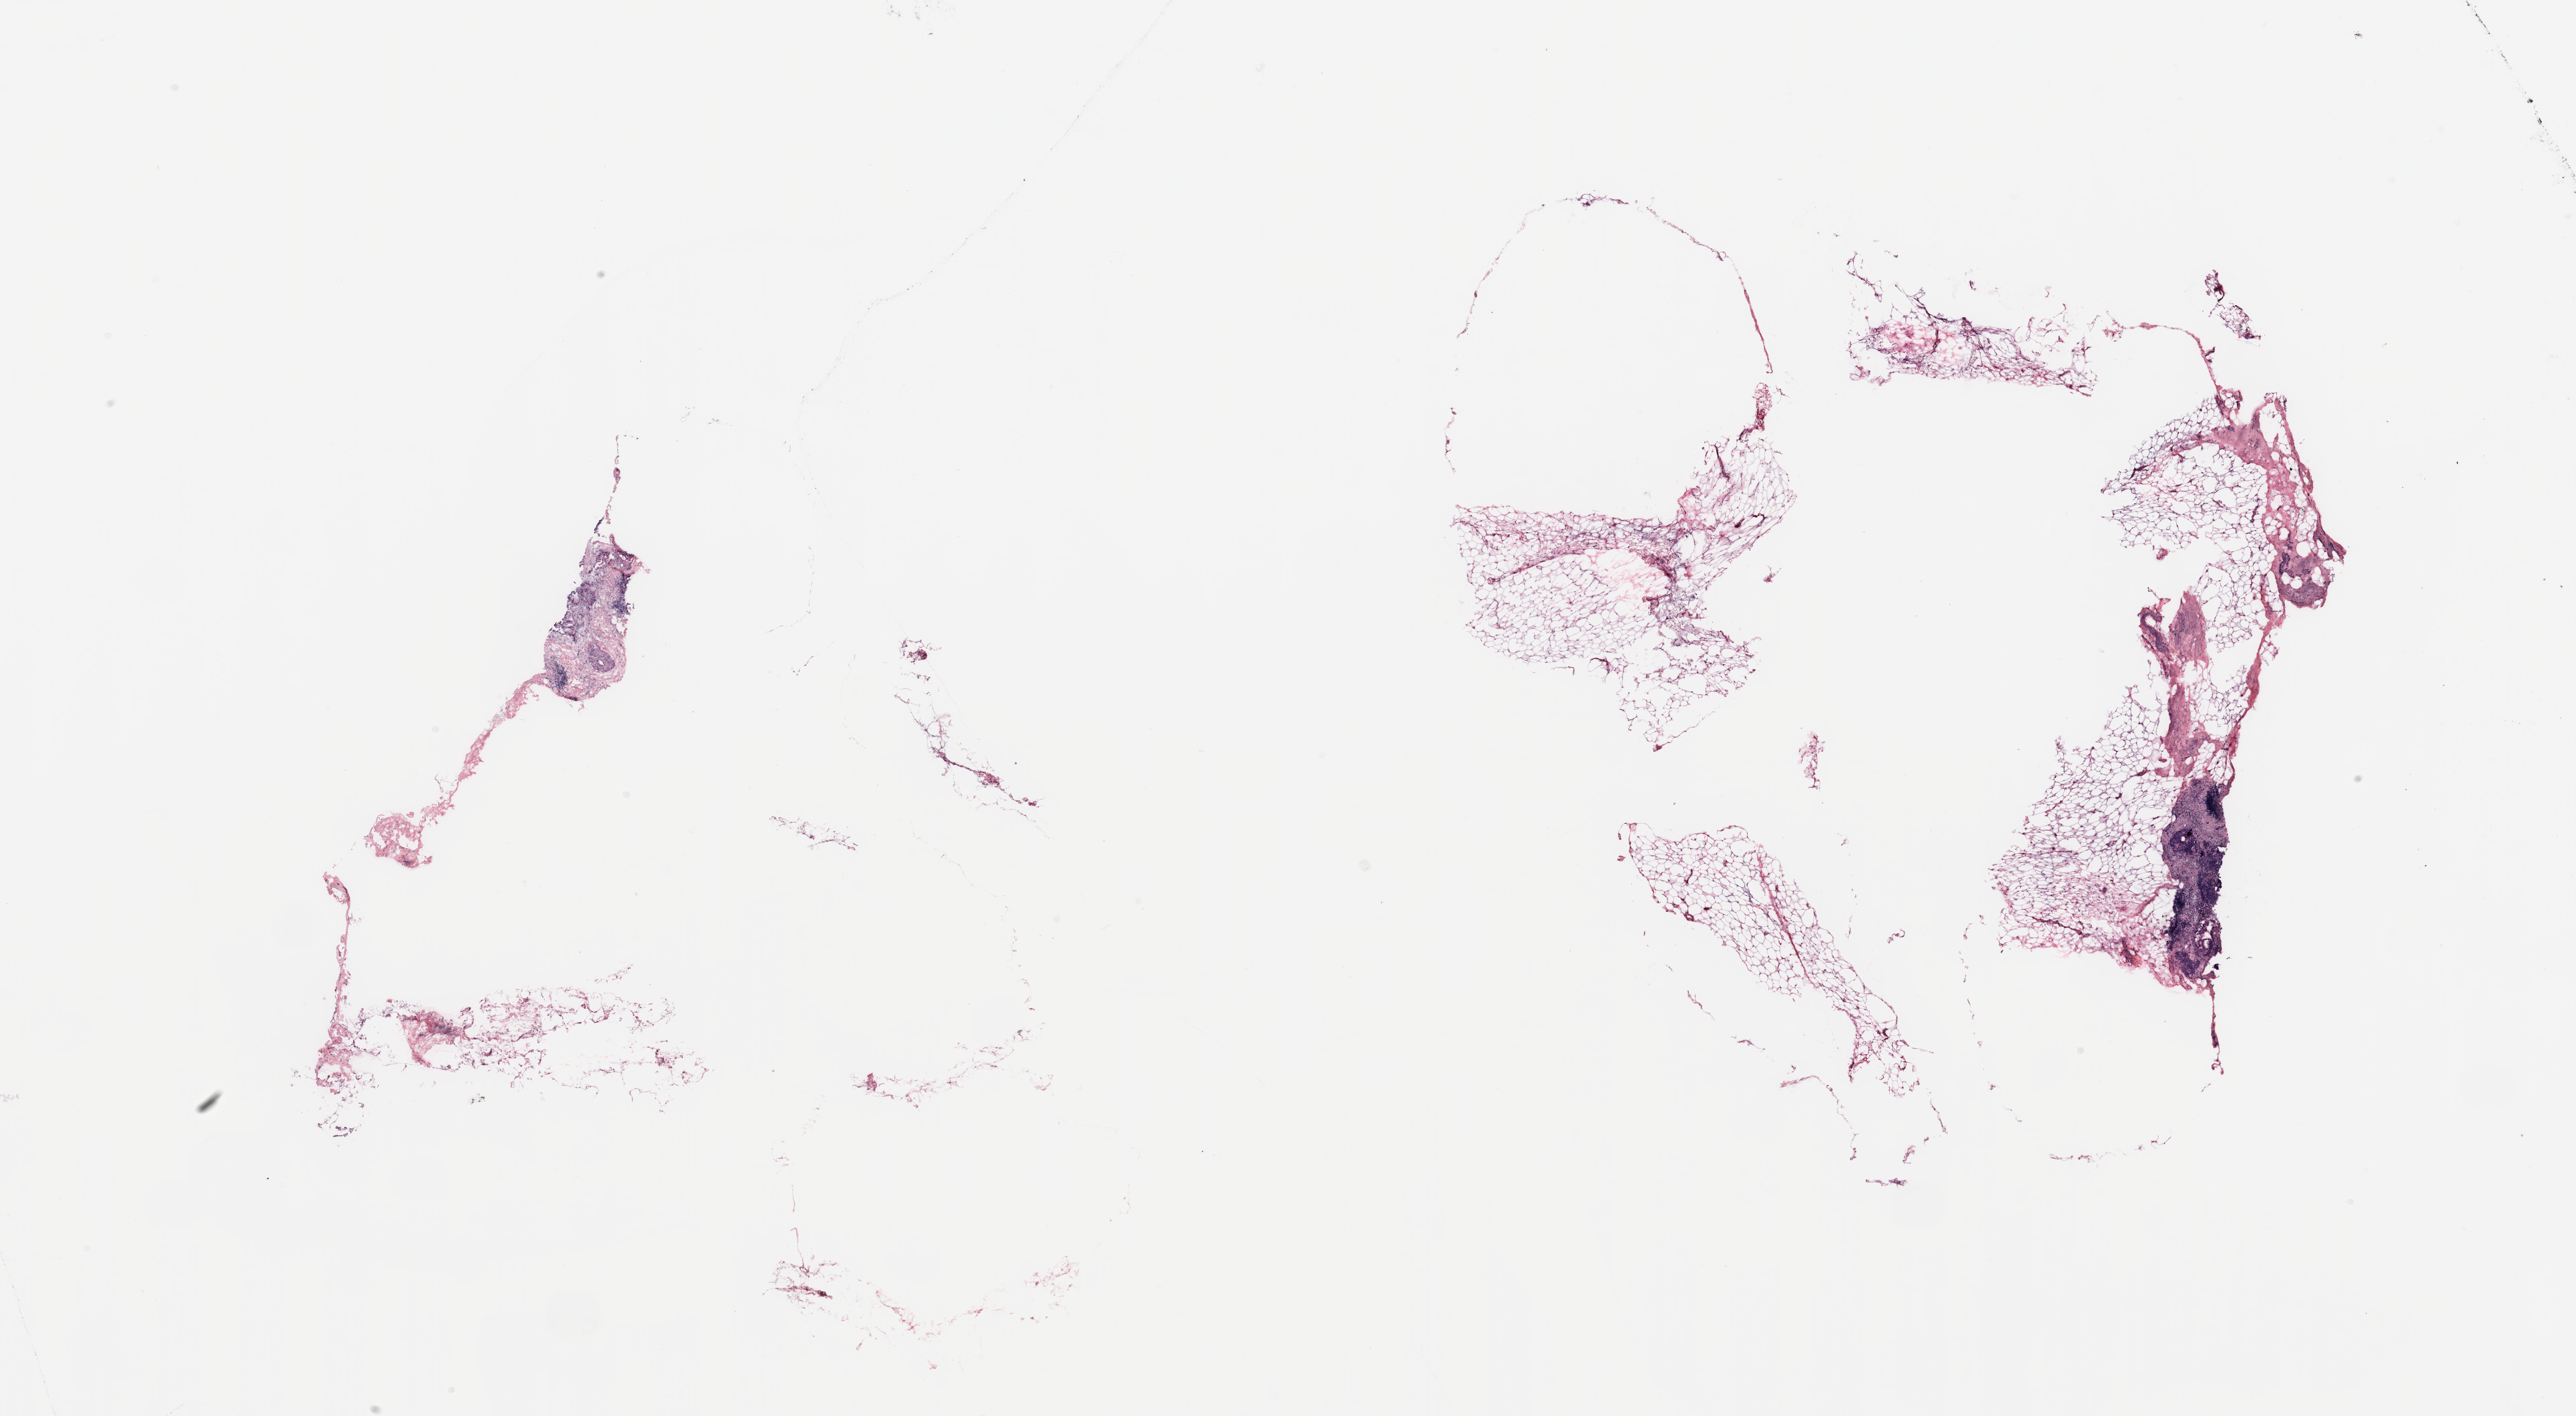
H&E-stained whole-slide image — whole scanned area (about 30.5 x 16.8 mm) shown as a low-resolution overview; tumour tissue sample, breast. 62-year-old female patient.
• AJCC pathologic stage: IIB
• diagnosis: Infiltrating duct carcinoma, NOS